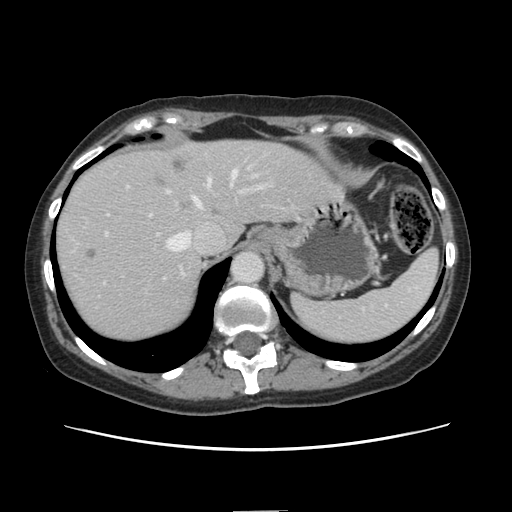
Contrast-enhanced abdominal CT, one axial slice; position 112 of 141 along the scan axis; intravenous contrast given; soft-tissue window (W 400 / L 40 HU); 2.5 mm slice thickness; 512 × 512 image matrix, field of view 350 × 350 mm. Female patient, age 63 years. Case-level facts recorded for this patient, not image findings: diagnosis: colorectal cancer liver metastases, imaged before liver resection; multiple liver metastases: yes; largest metastasis: 3.2 cm; disease in both lobes: yes.
Structures marked on this image (outlined manually by an expert reader):
- hepatic veins: bounding box <167,170,237,251> (left, top, right, bottom; pixels)
- liver: <56,140,337,343>
- planned liver remnant (the part of the liver to remain after resection): <194,141,340,242>
- portal vein (with intrahepatic branches): <234,164,253,192>
- liver metastasis: <152,174,165,187>